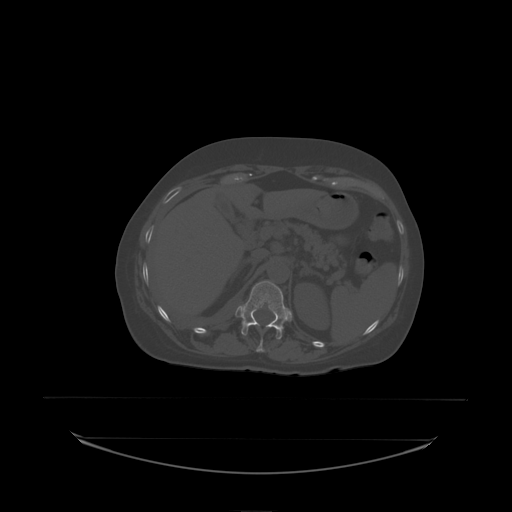
CT including the spine, one axial slice; position 96 of 242 along the scan axis; bone window (W 1800 / L 400 HU); 2.5 mm slice thickness; 512 × 512 image matrix, field of view 500 × 500 mm. Female patient, age 53 years. From the clinical record (not read from this slice): primary cancer: lung; vertebrae with lytic lesions (as recorded): T7, L1.
Annotated regions visible in this slice (semi-automatic segmentation, software-assisted and operator-edited):
- T12 vertebra: box from (x=241, y=281) to (x=289, y=336) px